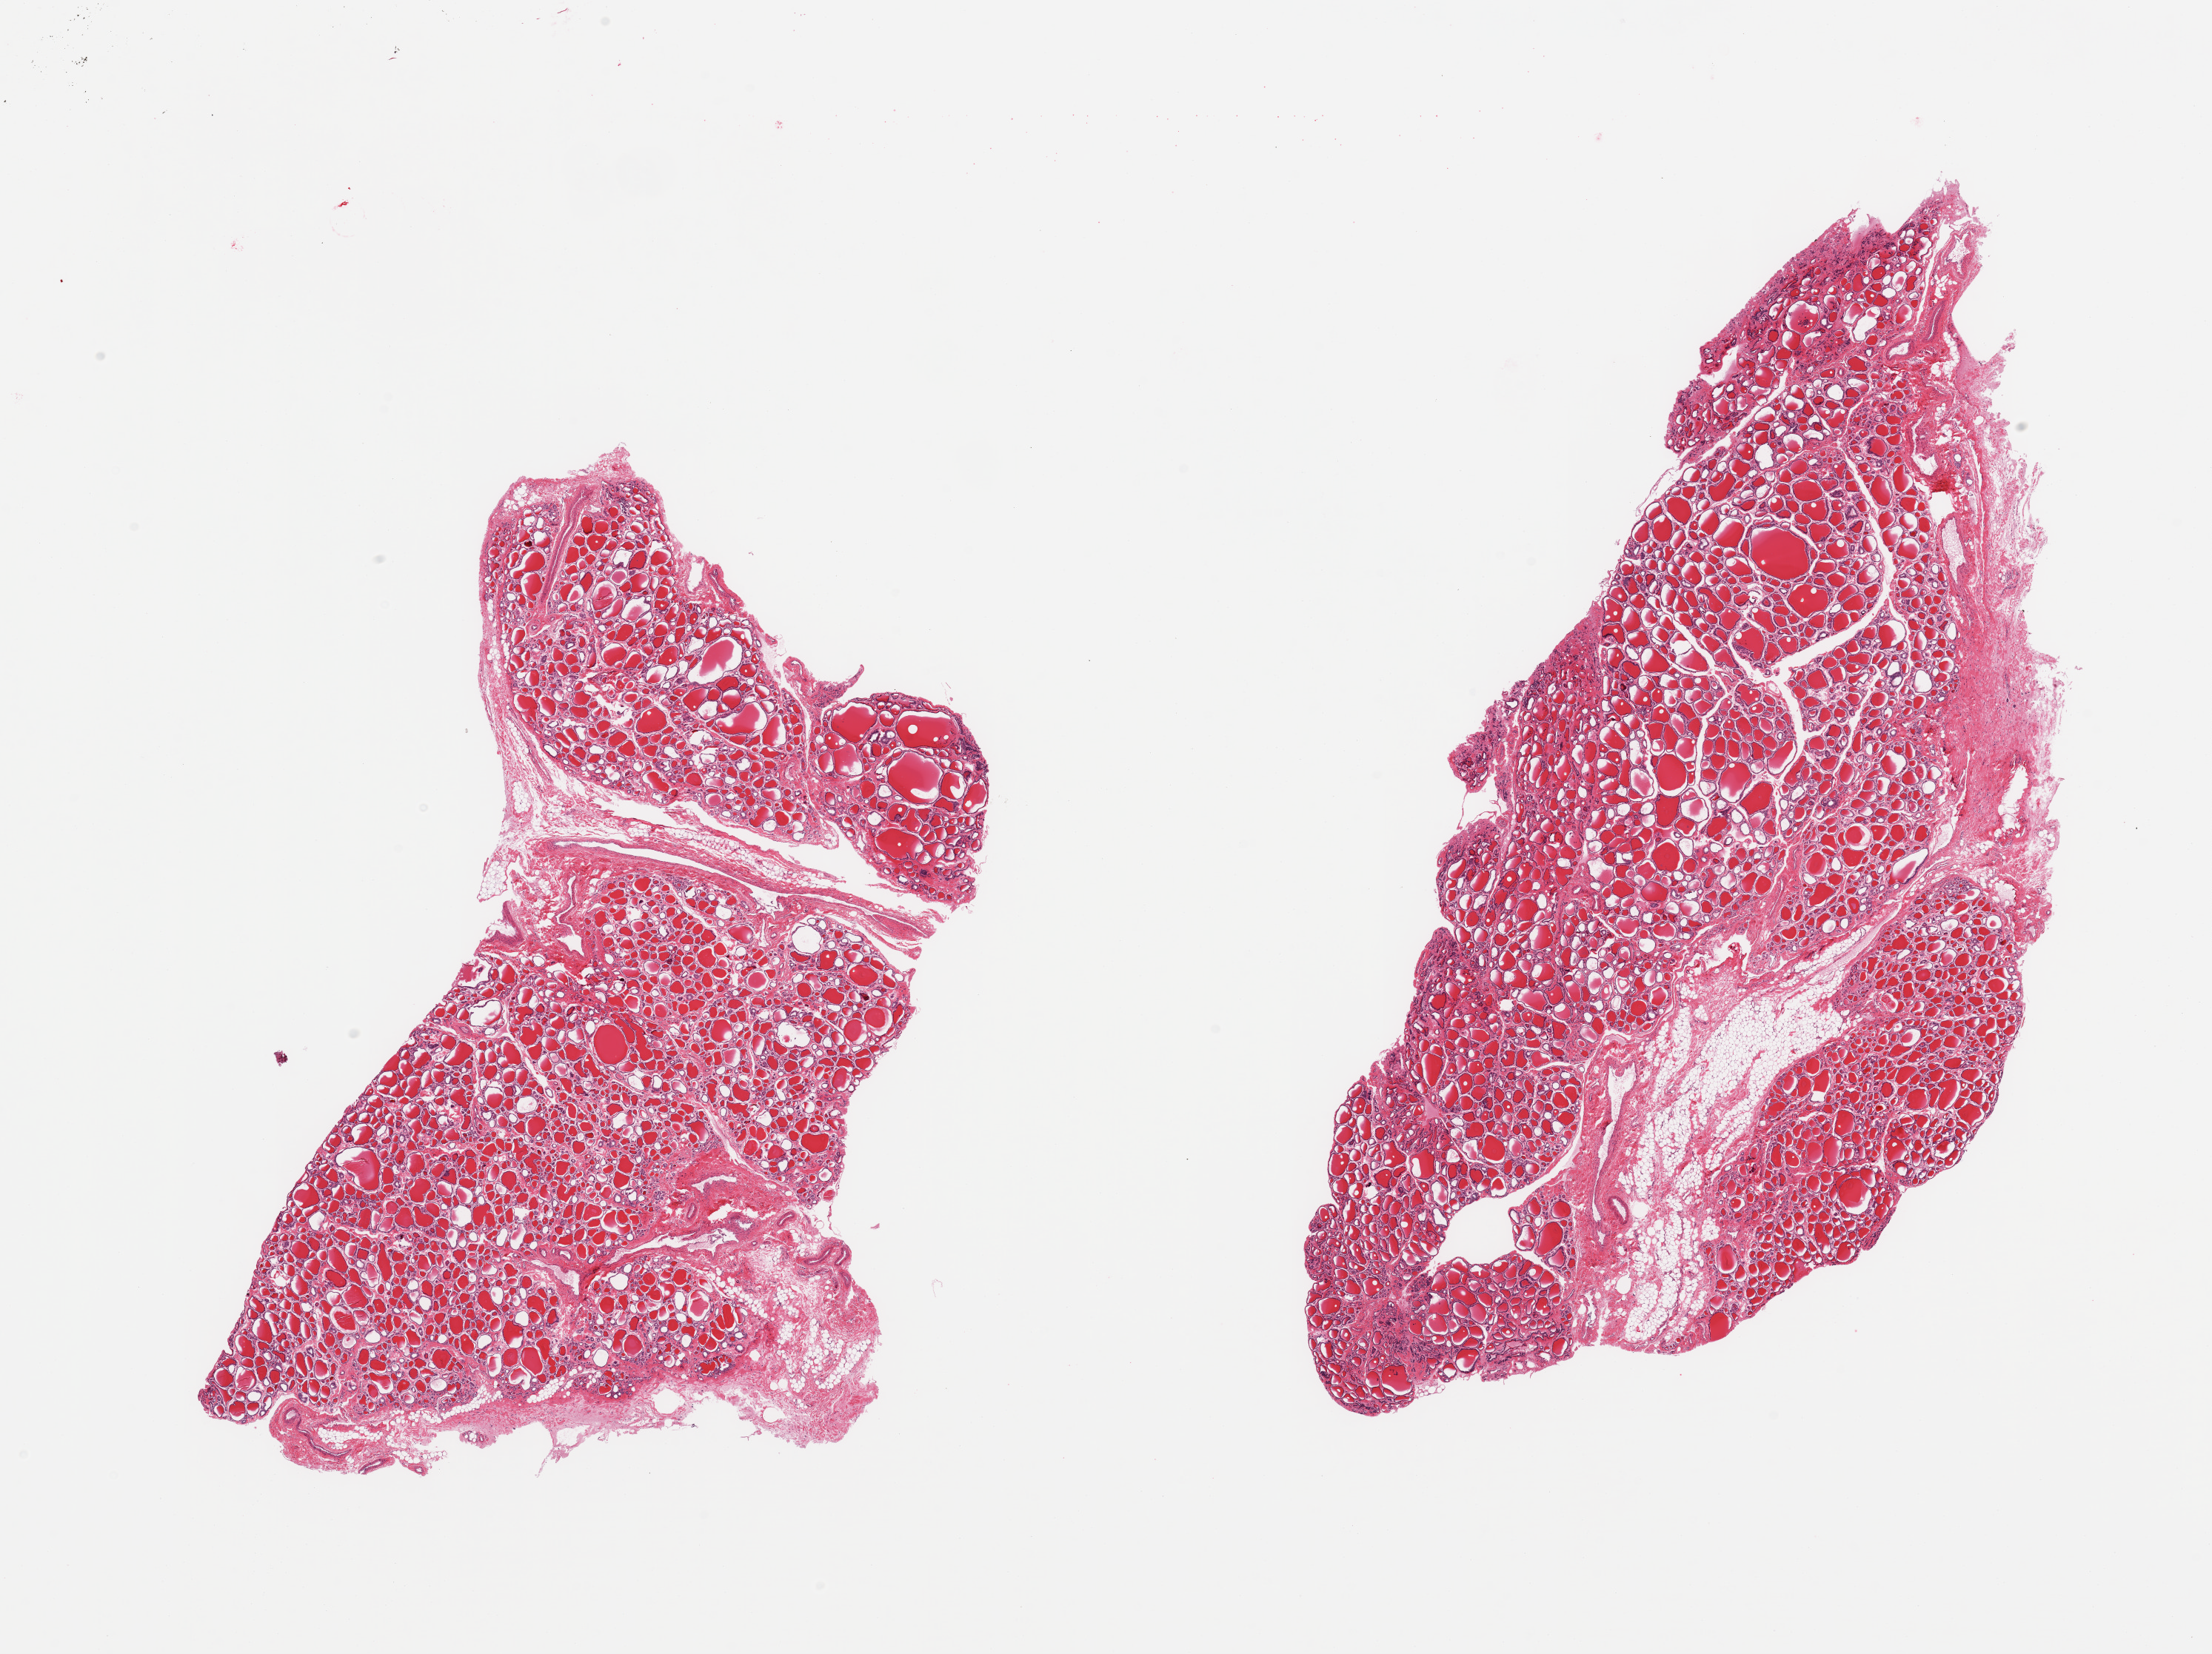
Haematoxylin and eosin whole-slide image — a low-resolution overview of the entire scanned area, about 23.6 x 17.7 mm (acquisition: 20x scan), PAXgene-fixed paraffin-embedded (PFPE) section, sampled site (target tissue): thyroid, donor tissue sample. Female donor.
Pathologist's review note for this sample: 2 pieces, ~10-15% adherent fat/vascular elements.